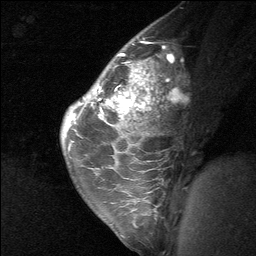
Breast MRI (dynamic contrast-enhanced), one sagittal slice. Slice 45 of 64 in the series (ordered by position). Dynamic contrast-enhanced study with each time point stored as its own series, time point 2 of 3 at this slice position (early post-contrast, ordered by acquisition time). 1.5 T. TE 4.8 ms, TR 27 ms. 2 mm slice thickness. 256 × 256 image matrix. Patient: female, 26 years. Case-level facts recorded for this patient, not image findings: setting: breast cancer imaged before/during neoadjuvant chemotherapy; receptor status: HR-positive, HER2-negative.
Annotated regions visible in this slice (semi-automatically segmented with operator editing):
- analysis volume of interest (the breast-tissue region the enhancement analysis was run in; not a lesion): bounding box [x1, y1, x2, y2] px = [86, 43, 174, 138]
- tumour enhancement mask (voxels above the 90 % enhancement threshold inside the analysis volume of interest): [95, 53, 157, 116]